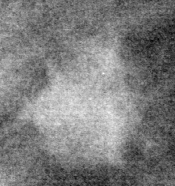
Crop from a digitized film mammogram around one marked abnormality, right breast, MLO view, BI-RADS breast density category 1 (scale 1–4).
Mass, shape round, margins circumscribed; BI-RADS assessment category 2; pathology (as recorded): benign.